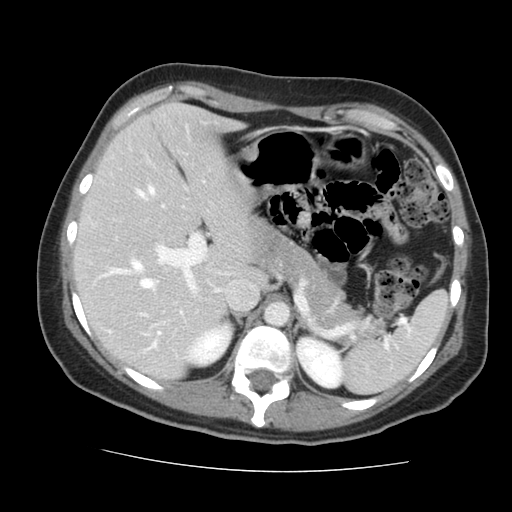
Contrast-enhanced abdominal CT, one axial slice. Position 98 of 144 along the scan axis. Intravenous contrast given. Soft-tissue window (W 400 / L 40 HU). 512 × 512 image matrix, field of view 333 × 333 mm. Female patient, age 46 years. Case-level facts recorded for this patient, not image findings: diagnosis: colorectal cancer liver metastases, imaged before liver resection; multiple liver metastases: no; largest metastasis: 2.8 cm; disease in both lobes: no.
Structures marked on this image (outlined manually by an expert reader):
- hepatic veins: bounding box <137,187,218,291> (left, top, right, bottom; pixels)
- liver: <77,105,262,378>
- planned liver remnant (the part of the liver to remain after resection): <77,105,262,378>
- portal vein (with intrahepatic branches): <105,233,207,348>